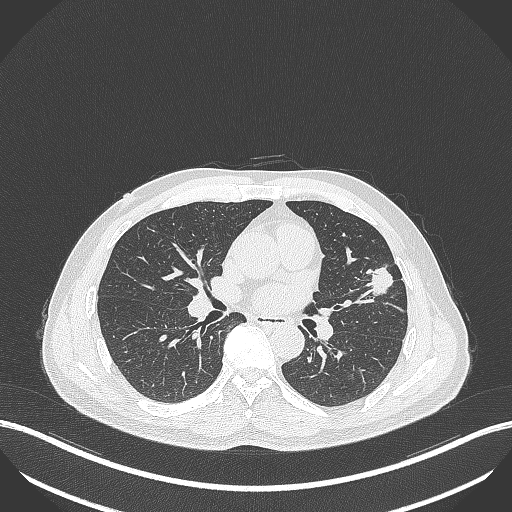
Chest CT, one axial slice; slice 210 of 418 in the series (ordered by position); lung window (W 1500 / L -600 HU); 1 mm slice thickness; 512 × 512 image matrix, field of view 400 × 400 mm. Male patient, age 55 years. Case-level facts recorded for this patient, not image findings: clinical TNM (as recorded): T1c N0 M0.
Annotated regions visible in this slice (bounding box drawn by a radiologist):
- lung tumour (recorded histology: adenocarcinoma): bounding box (x1, y1, x2, y2) in pixels: (366, 261, 398, 299)